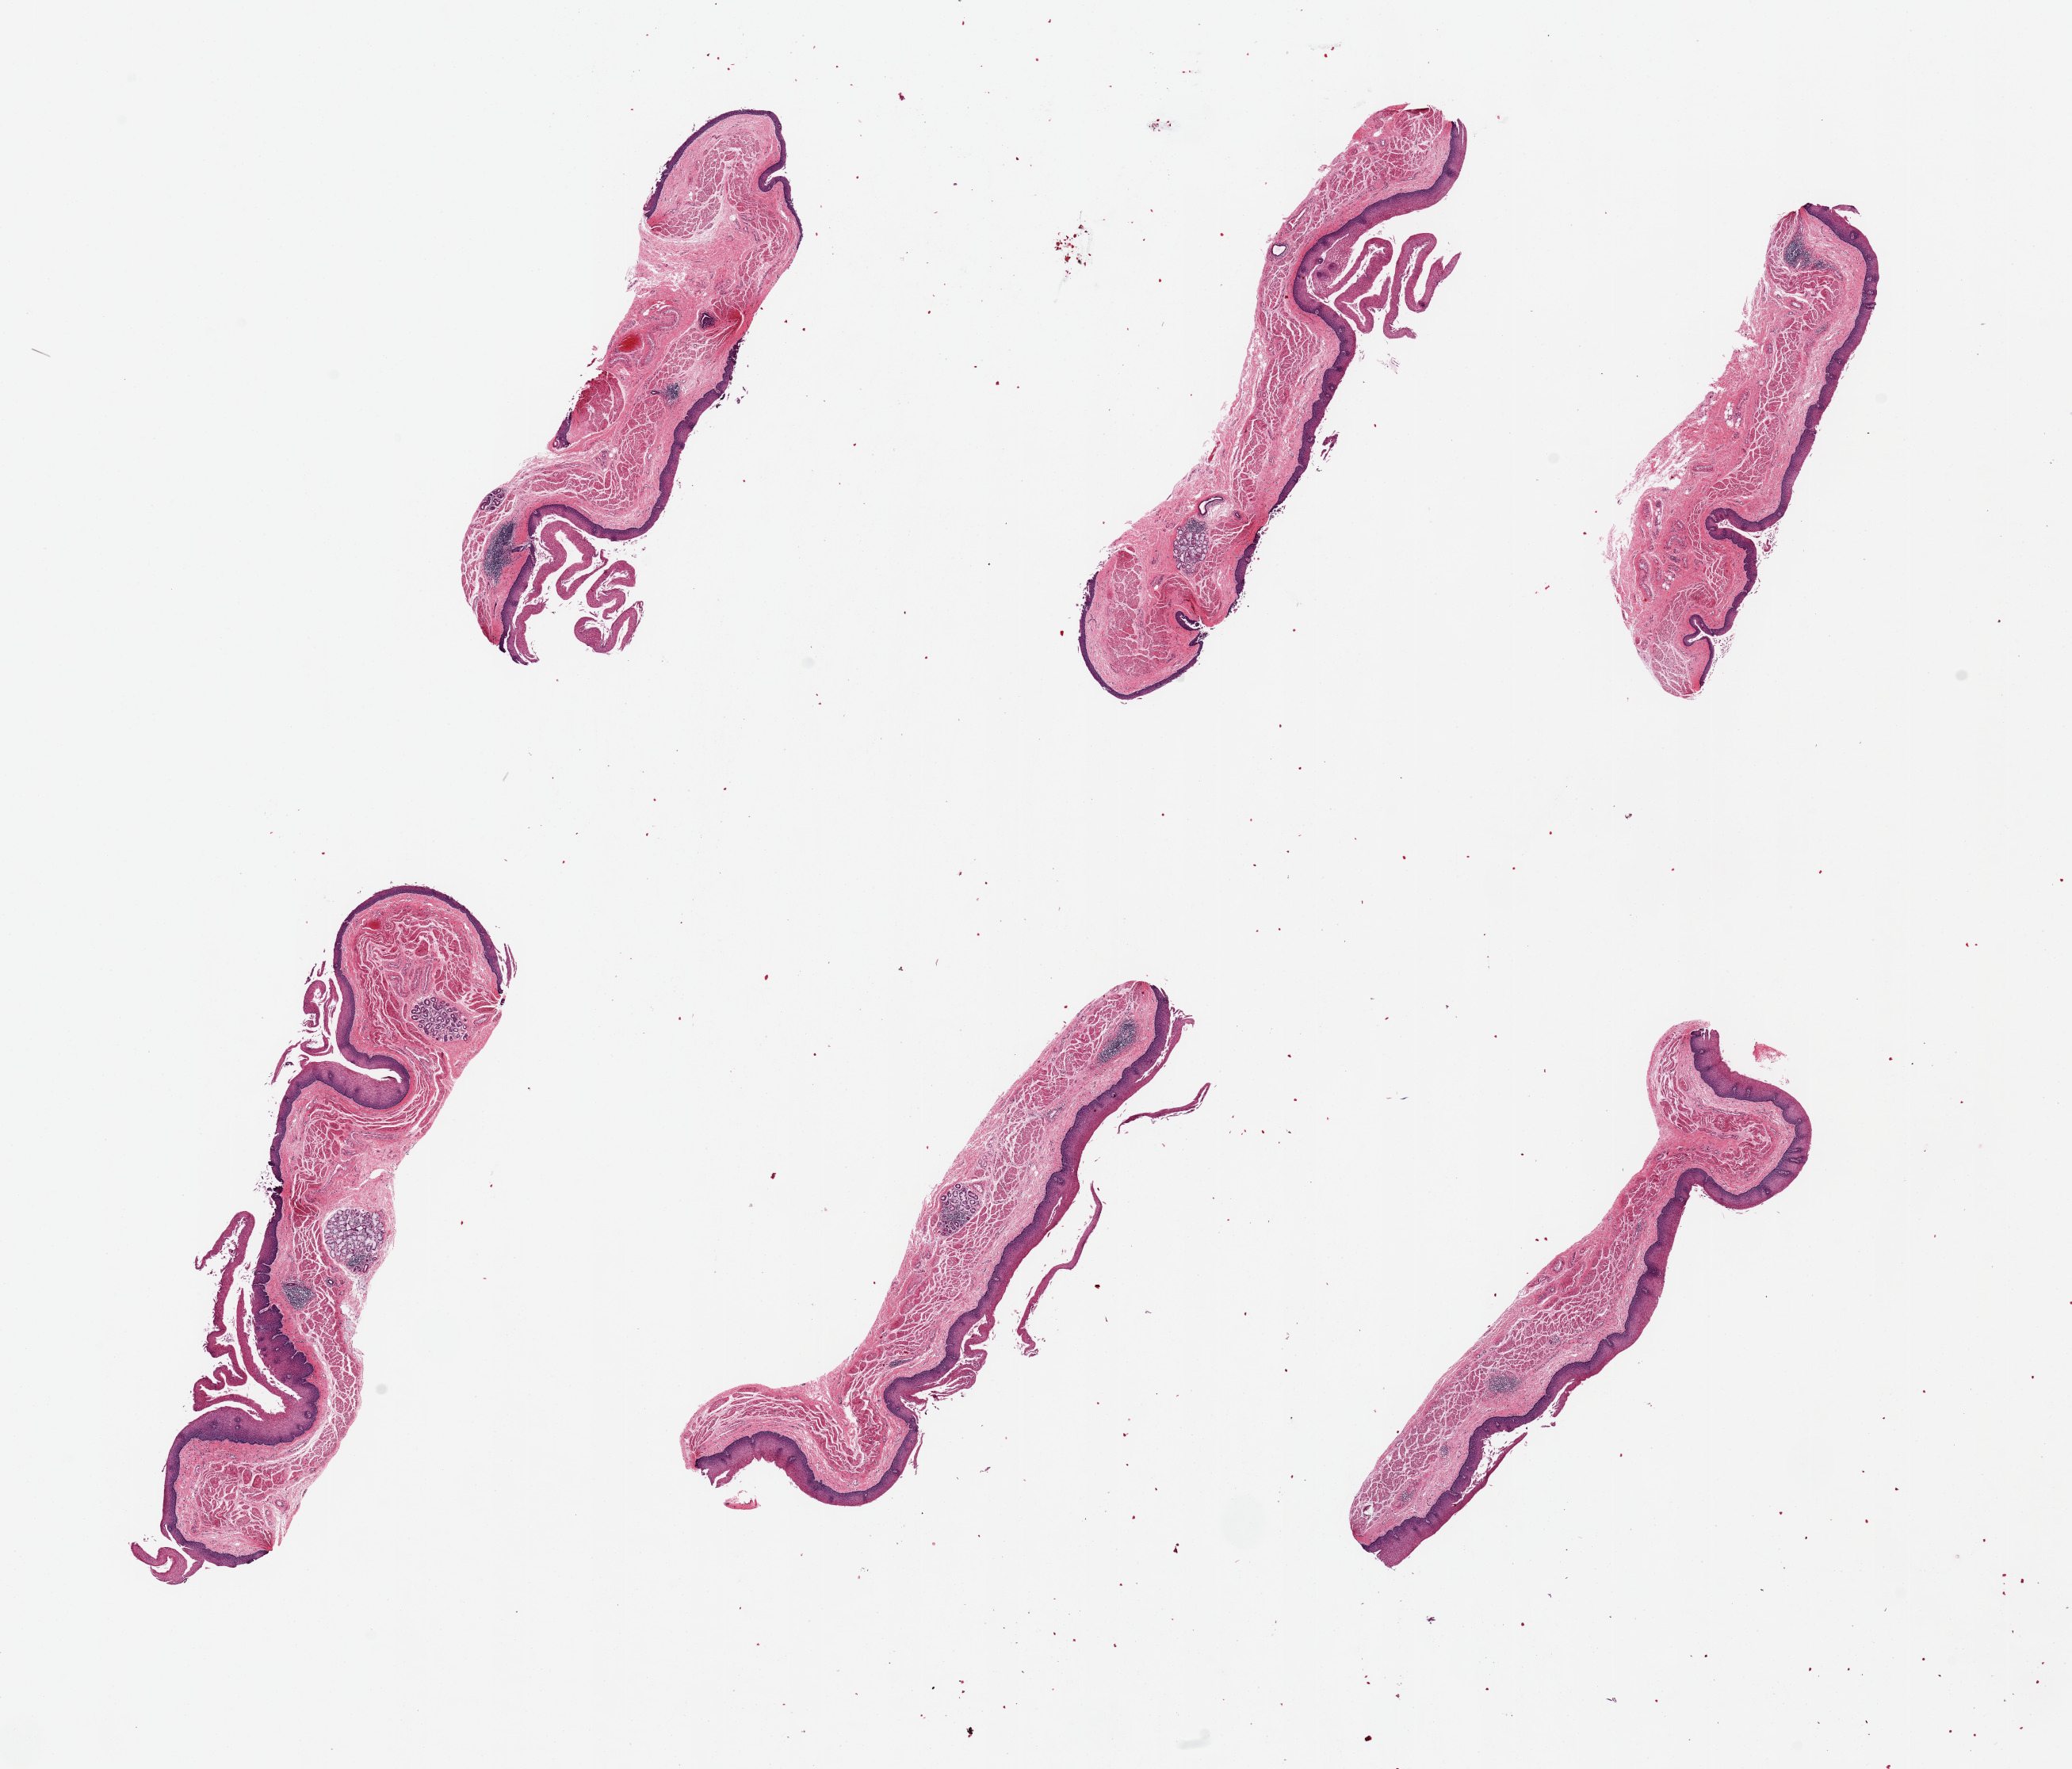
Digitized H&E-stained section, brightfield, low-resolution overview of the scanned area, about 20.7 x 17.7 mm (slide scanned at 20x). PAXgene-fixed paraffin-embedded (PFPE) section. Target tissue: esophageal mucous membrane. Tissue donor sample. Male donor.
* reviewer comment on this tissue sample: 6 pieces, up to 7x2mm; partly detached mucosa